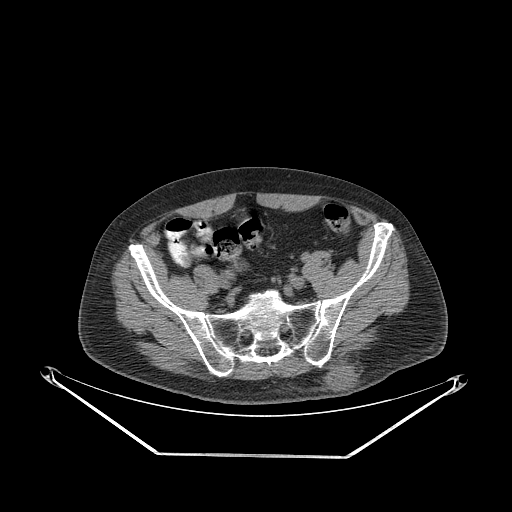
CT of an extremity soft-tissue mass (from a PET/CT study), one axial slice. Position 75 of 267 along the scan axis. Reconstruction kernel STANDARD. 140 kVp. Soft-tissue window (W 400 / L 40 HU). 3.75 mm slice thickness. 512 × 512 image matrix, field of view 500 × 500 mm. Male patient. From the clinical record (not read from this slice): histological type: leiomyosarcoma; grade: intermediate; site of the primary tumour: left pelvis.
Annotated regions visible in this slice (expert contour drawn on MRI and transferred to this co-registered scan by the dataset authors):
- gross tumour volume (mass): bounding box <324,361,362,394> (left, top, right, bottom; pixels)